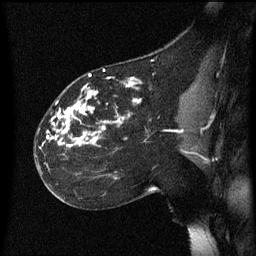
Breast MRI (dynamic contrast-enhanced), one sagittal slice; slice 33 of 60 in the series (ordered by position); dynamic contrast-enhanced series, image 2 of 3 at this slice position (ordered by acquisition); 1.5 T; TE 4.2 ms, TR 8.4 ms; 2.2 mm slice thickness; 256 × 256 image matrix. Patient: female, 35 years. From the clinical record (not read from this slice): setting: breast cancer imaged before/during neoadjuvant chemotherapy; receptor status: HER2-positive.
Annotated regions visible in this slice (semi-automatically segmented with operator editing):
- analysis volume of interest (the breast-tissue region the enhancement analysis was run in; not a lesion): bounding box [x1, y1, x2, y2] px = [35, 72, 178, 173]
- tumour enhancement mask (voxels above the 70 % enhancement threshold inside the analysis volume of interest): [40, 74, 142, 149]